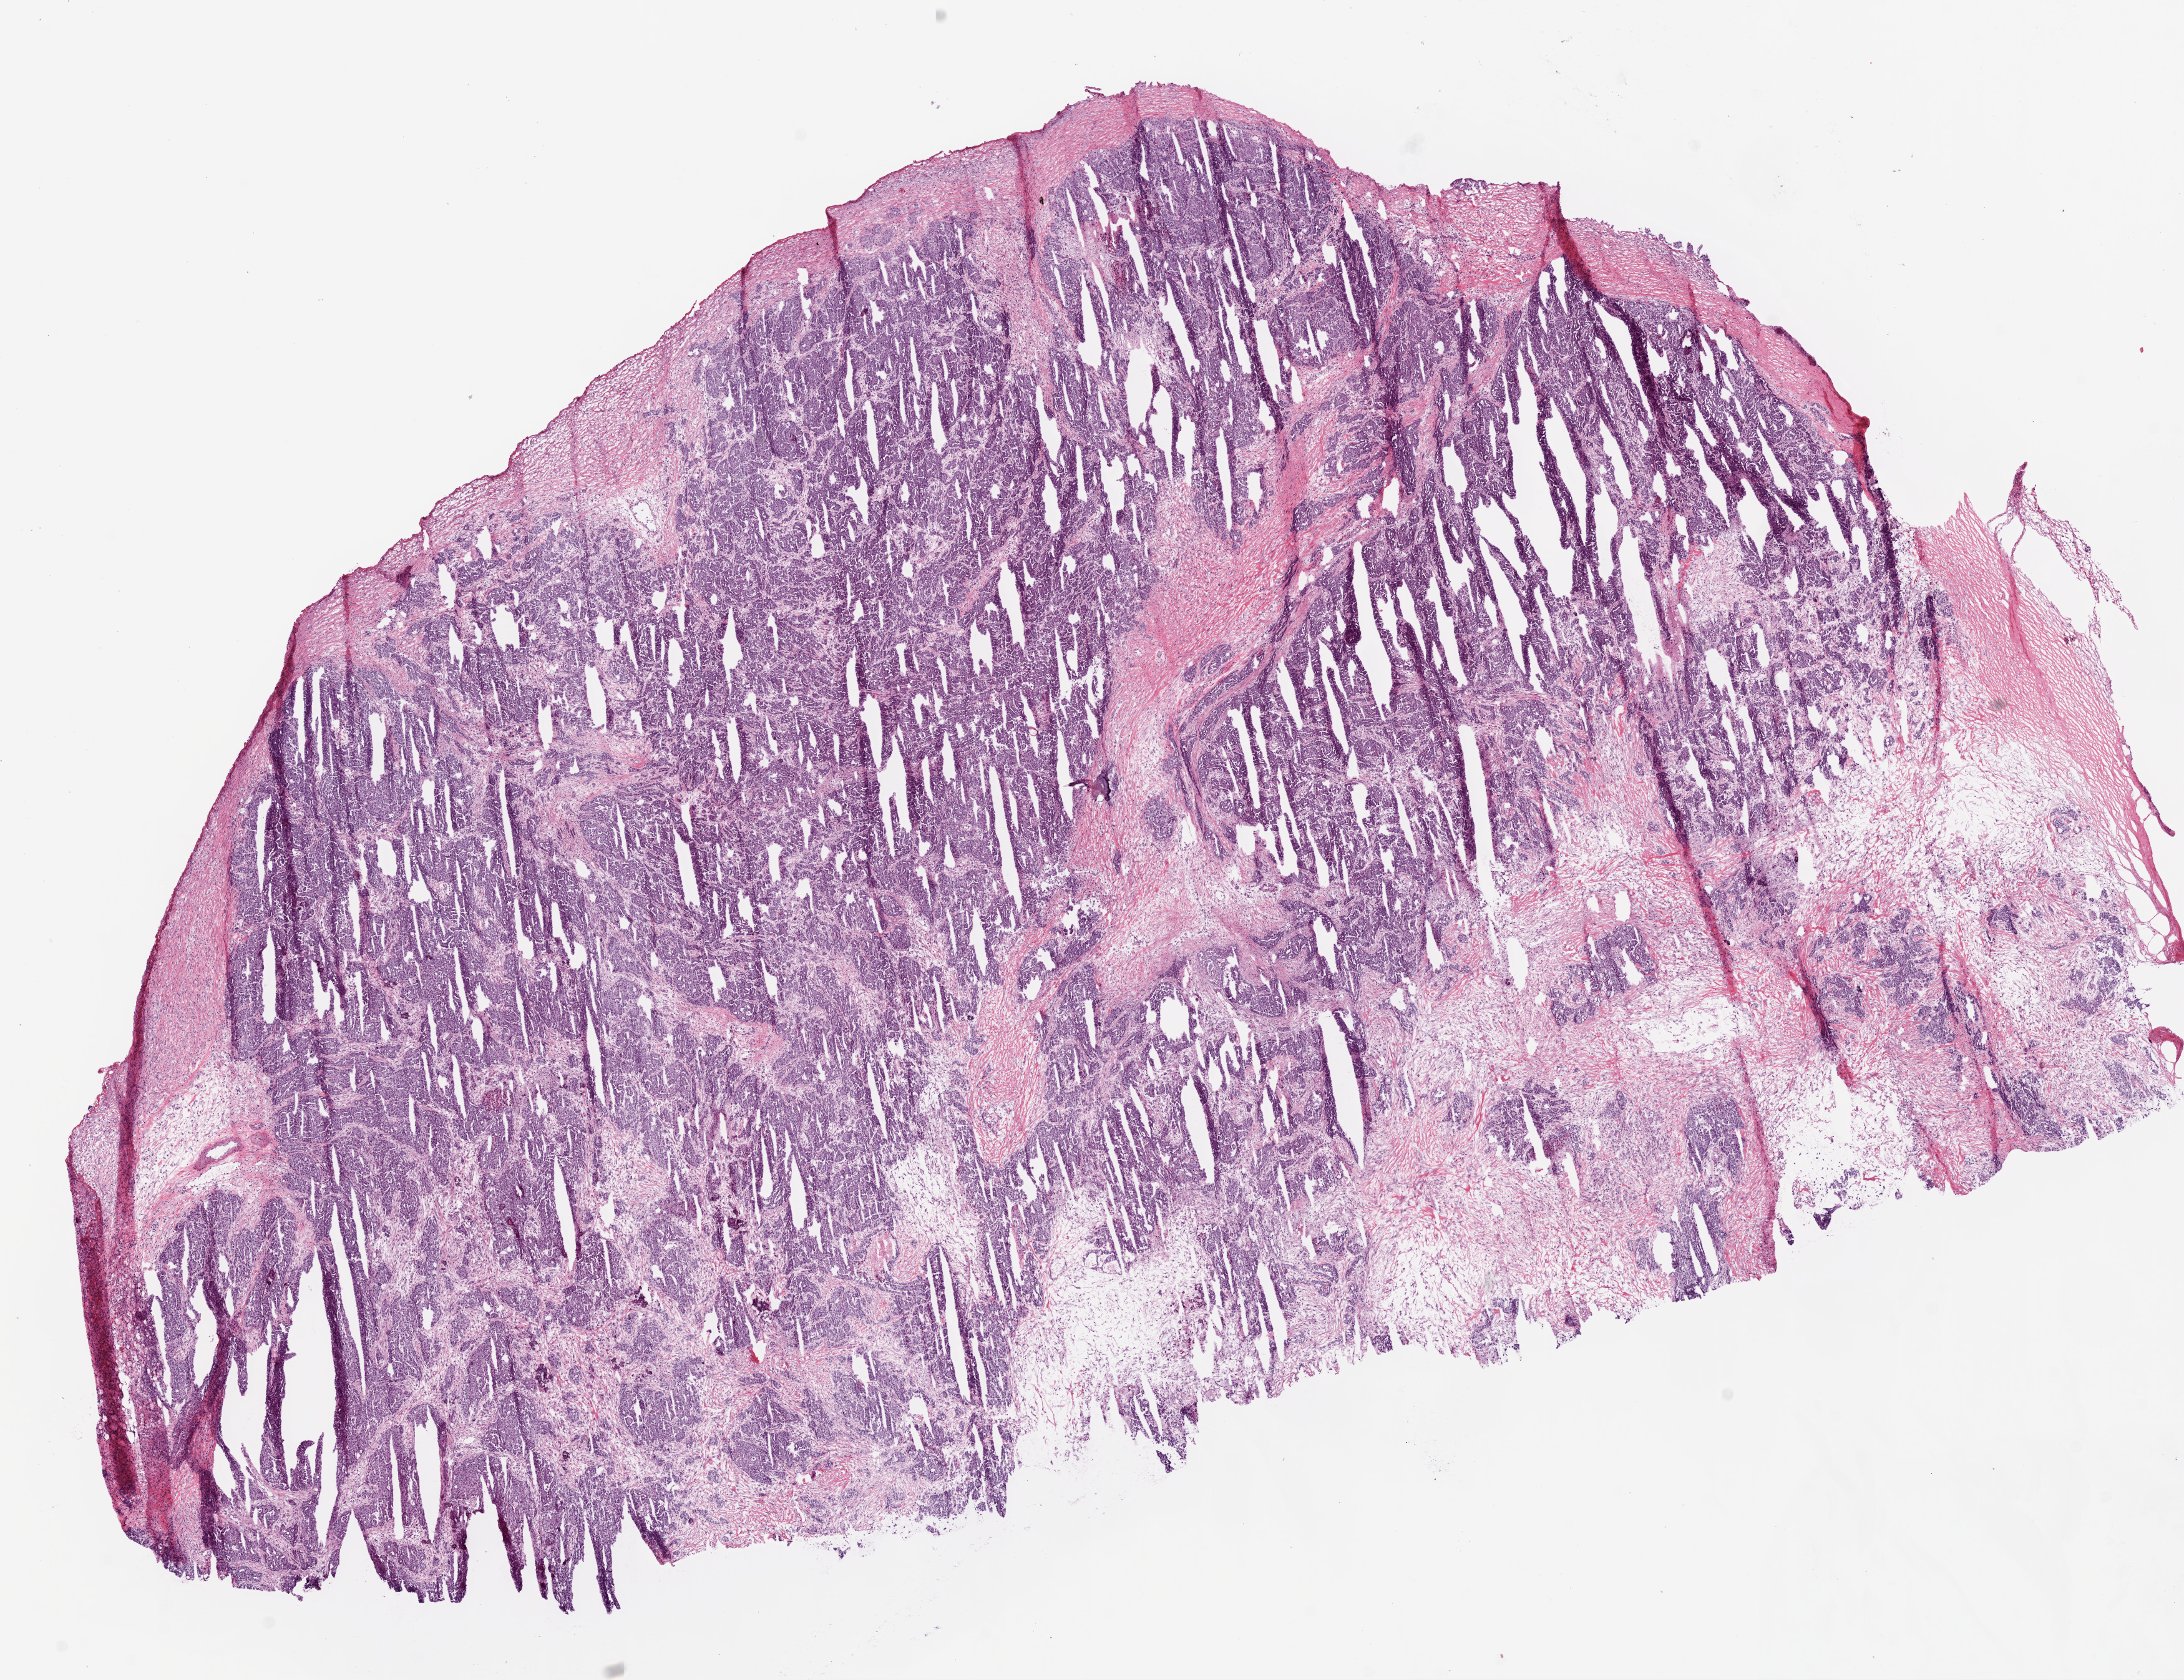
Digitized Hematoxylin and eosin (H&E) stained tissue section (whole slide), whole scanned area (about 14.0 x 10.8 mm, from a 20x scan) shown as a low-resolution overview; frozen section; primary tumour sample from the ovary. Female, age 57 years at initial diagnosis. Histologic grade: G3 (poorly differentiated). Composition of this section per pathologist review: tumour cells 70%, tumour nuclei 75%, normal cells 0%, stromal cells 25%, necrosis 5%.
* FIGO stage: IIIC
* diagnosis: Serous cystadenocarcinoma, NOS